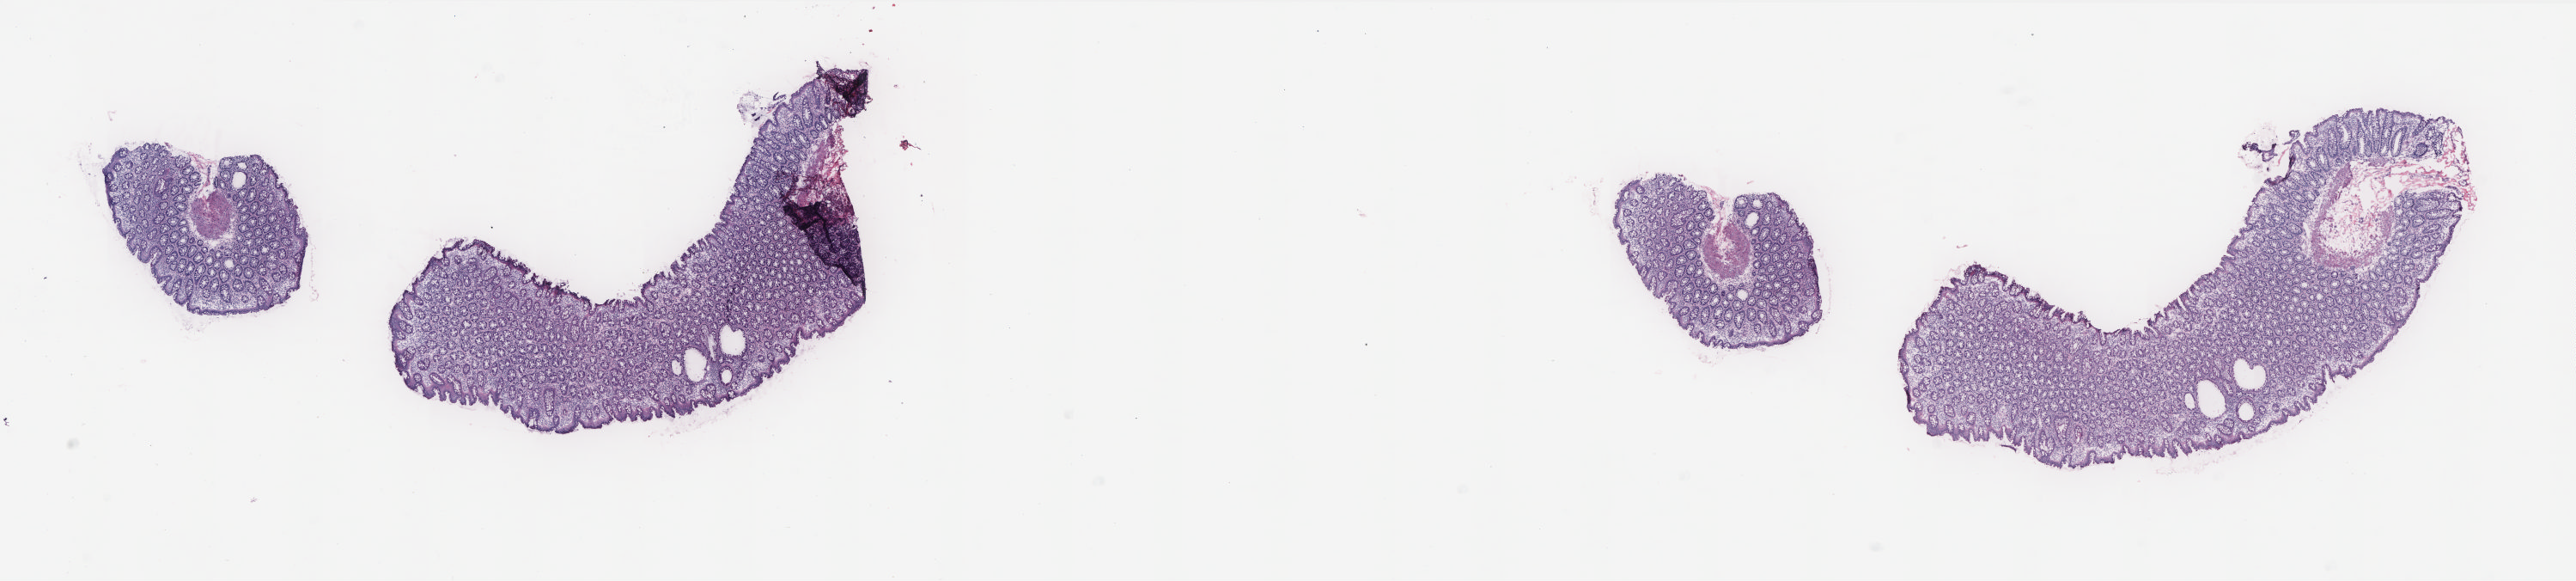
Digitized H&E tissue section (whole slide), a low-resolution overview of the entire scanned area, about 24.0 x 5.4 mm. Frozen section from the bottom of the tissue portion. Colon, solid tissue normal (non-tumour tissue) sample. Patient: female, age at initial diagnosis 80 years.
This section: solid tissue normal sample (biorepository sample class). Patient diagnosis: Adenocarcinoma, NOS (sigmoid colon).